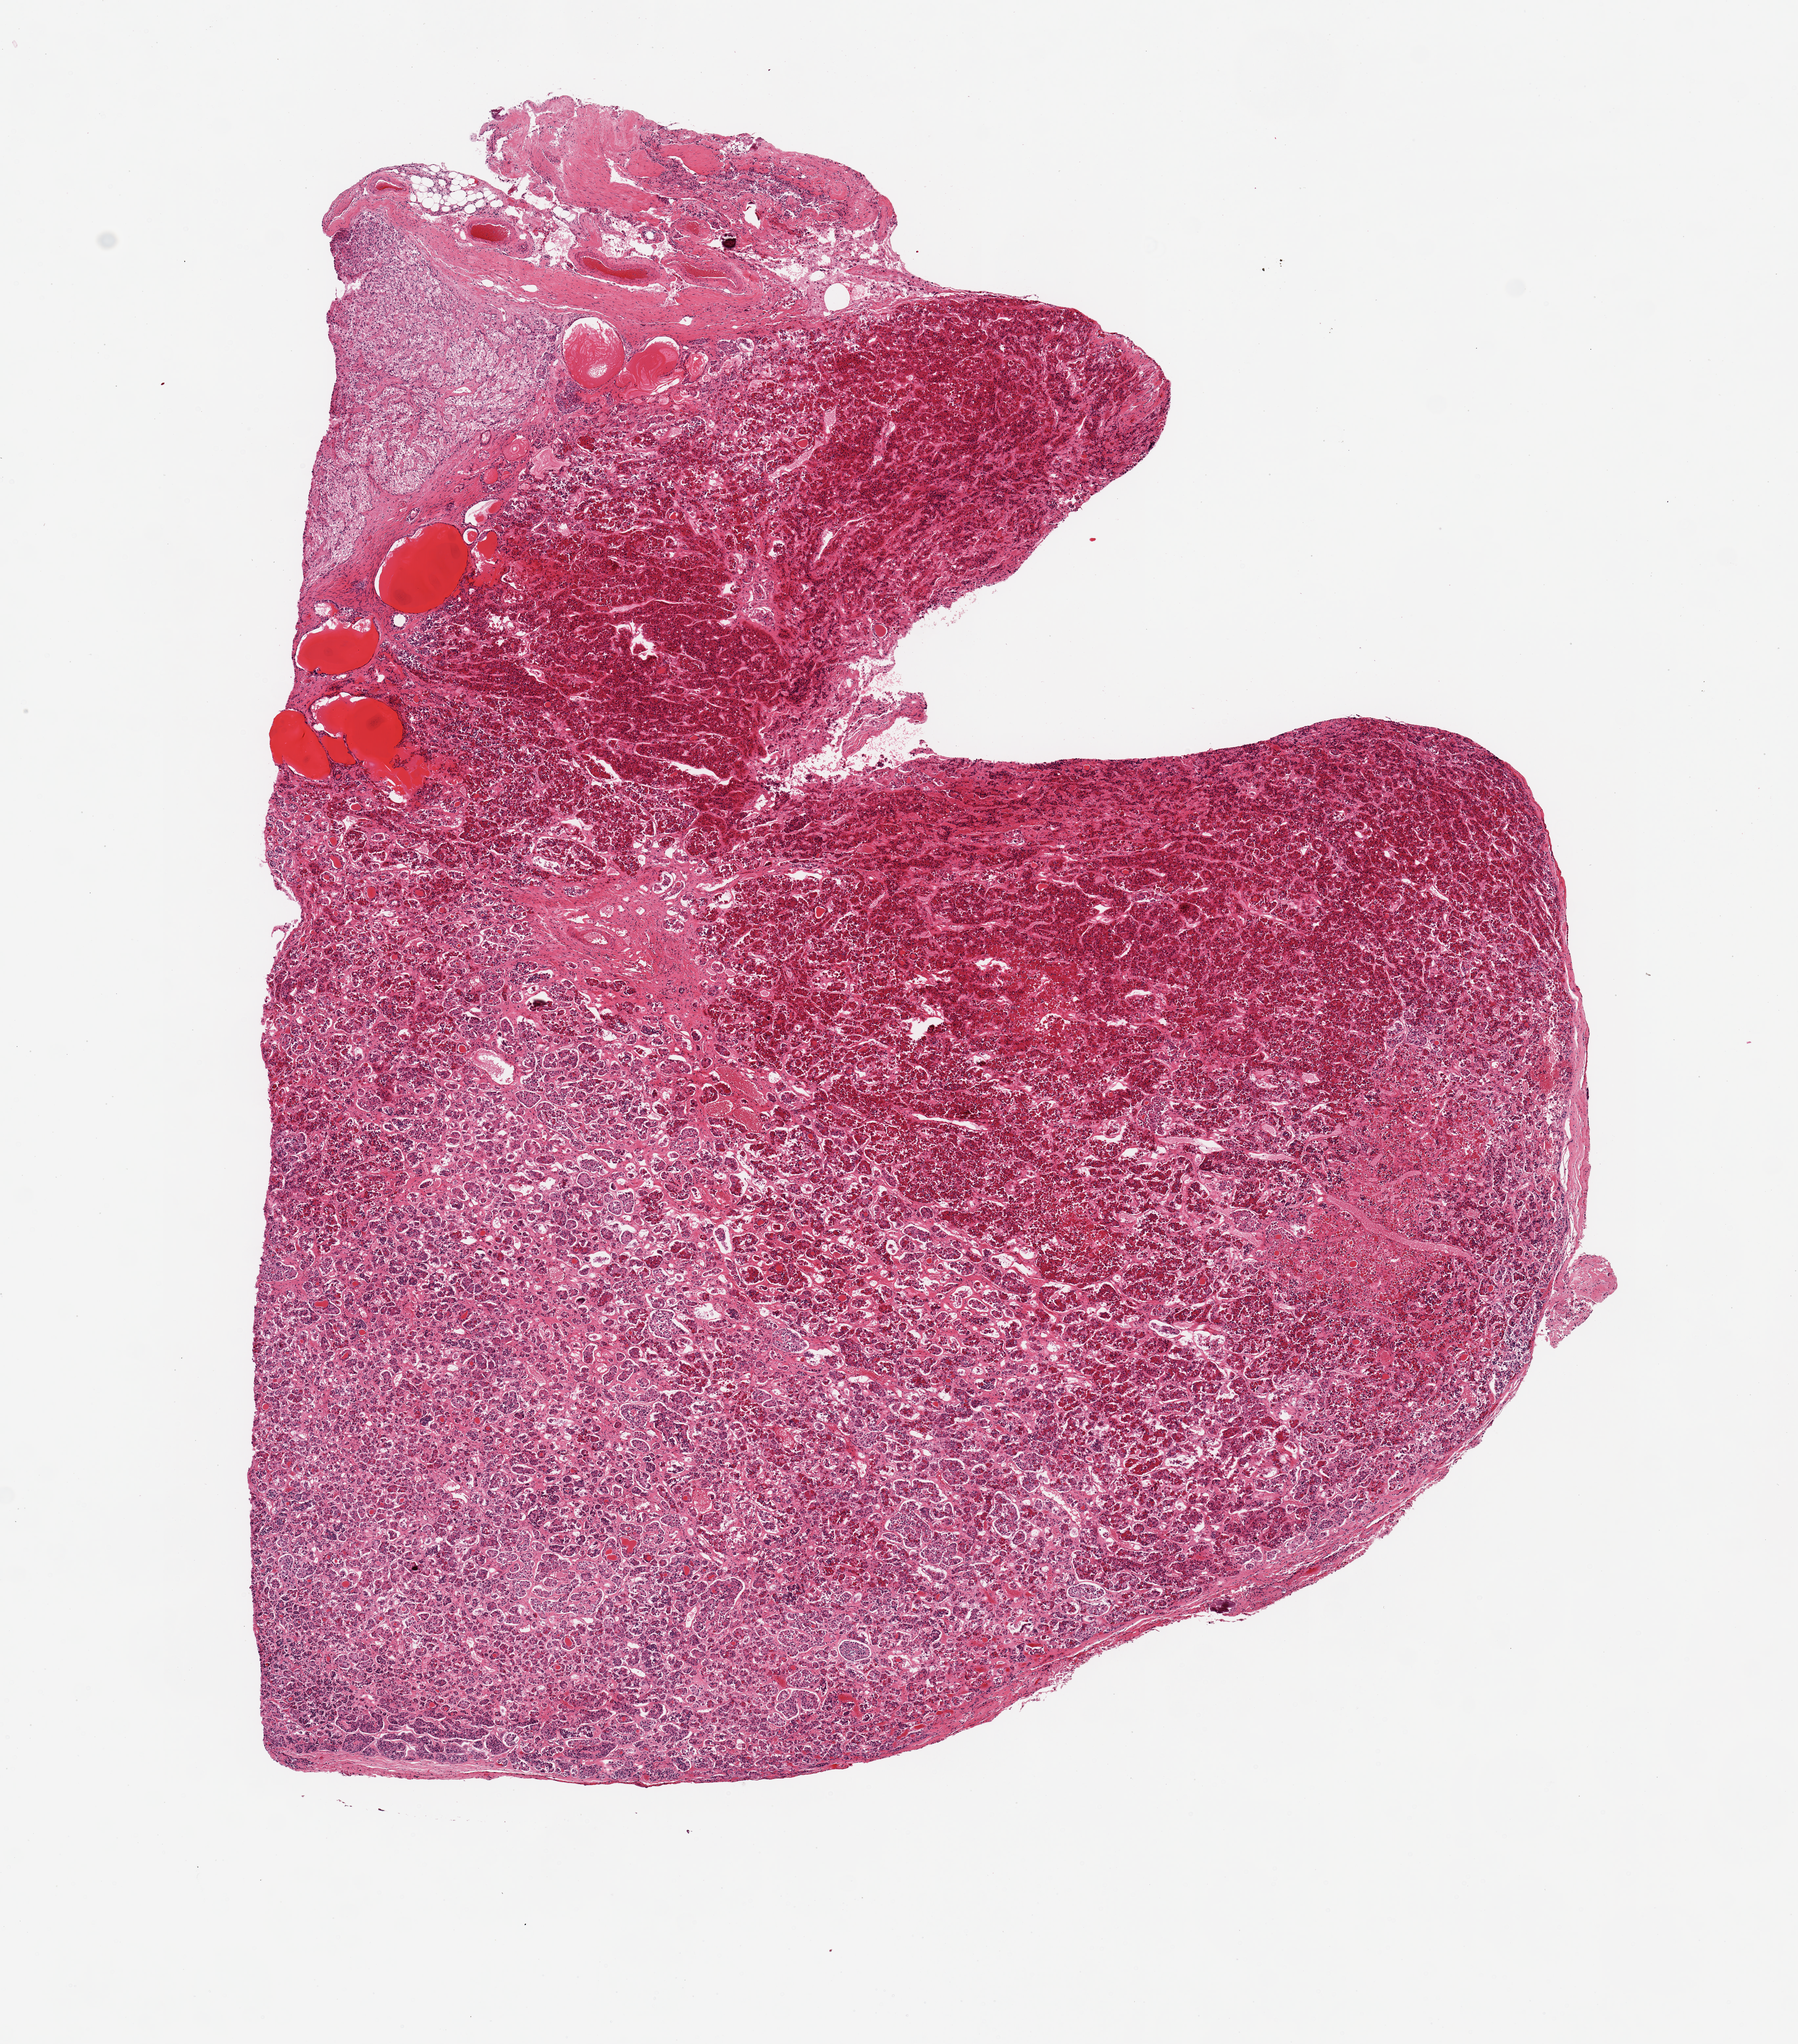
Whole-slide image, haematoxylin and eosin stain, brightfield — a low-resolution overview of the entire scanned area, about 10.8 x 12.3 mm (acquisition: 20x scan), PAXgene-fixed, paraffin-embedded tissue, sampled site (target tissue): pituitary, donor tissue sample. Donor sex: female.
Pathologist's review note for this sample: 1 piece, moderately autolyzed adenohypophysis.